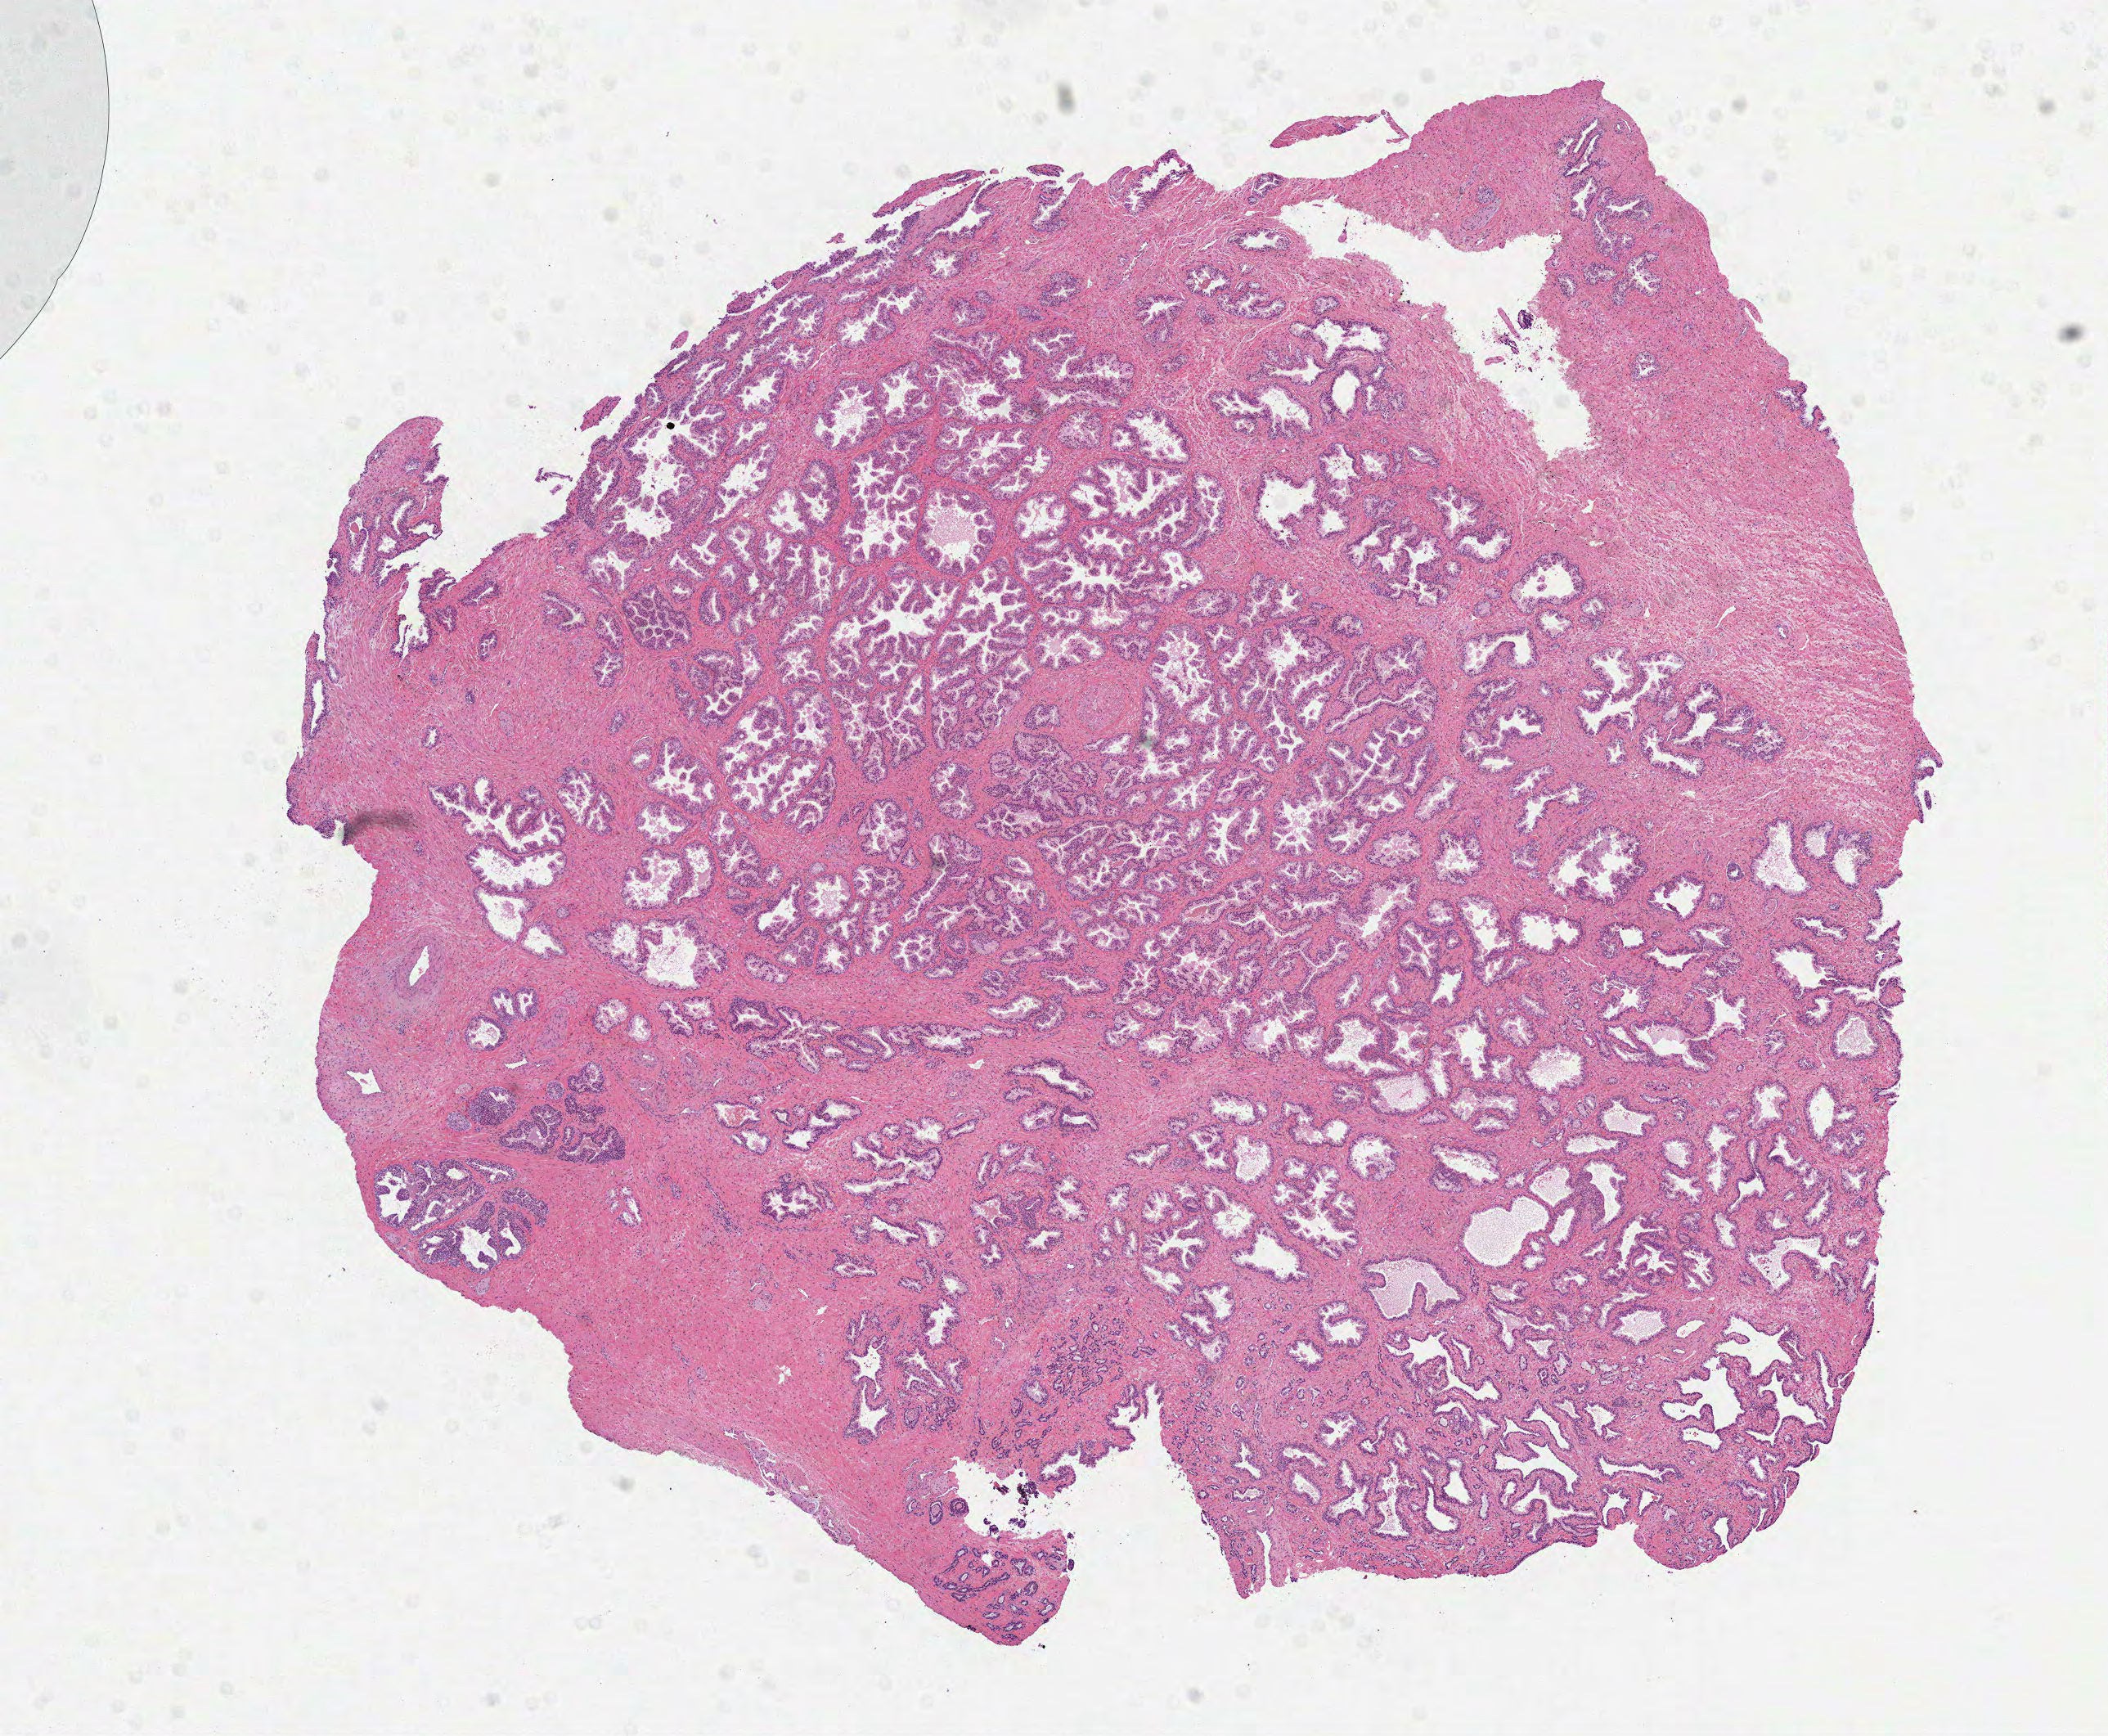
Whole-slide histology image, Hematoxylin and eosin (H&E) stained — a low-resolution overview of the entire scanned area, about 10.4 x 8.6 mm; formalin-fixed paraffin-embedded (FFPE) diagnostic section; sample: primary tumour, prostate. Male patient; age at initial diagnosis 50 years.
Histologic diagnosis: Acinar cell carcinoma (prostate gland).